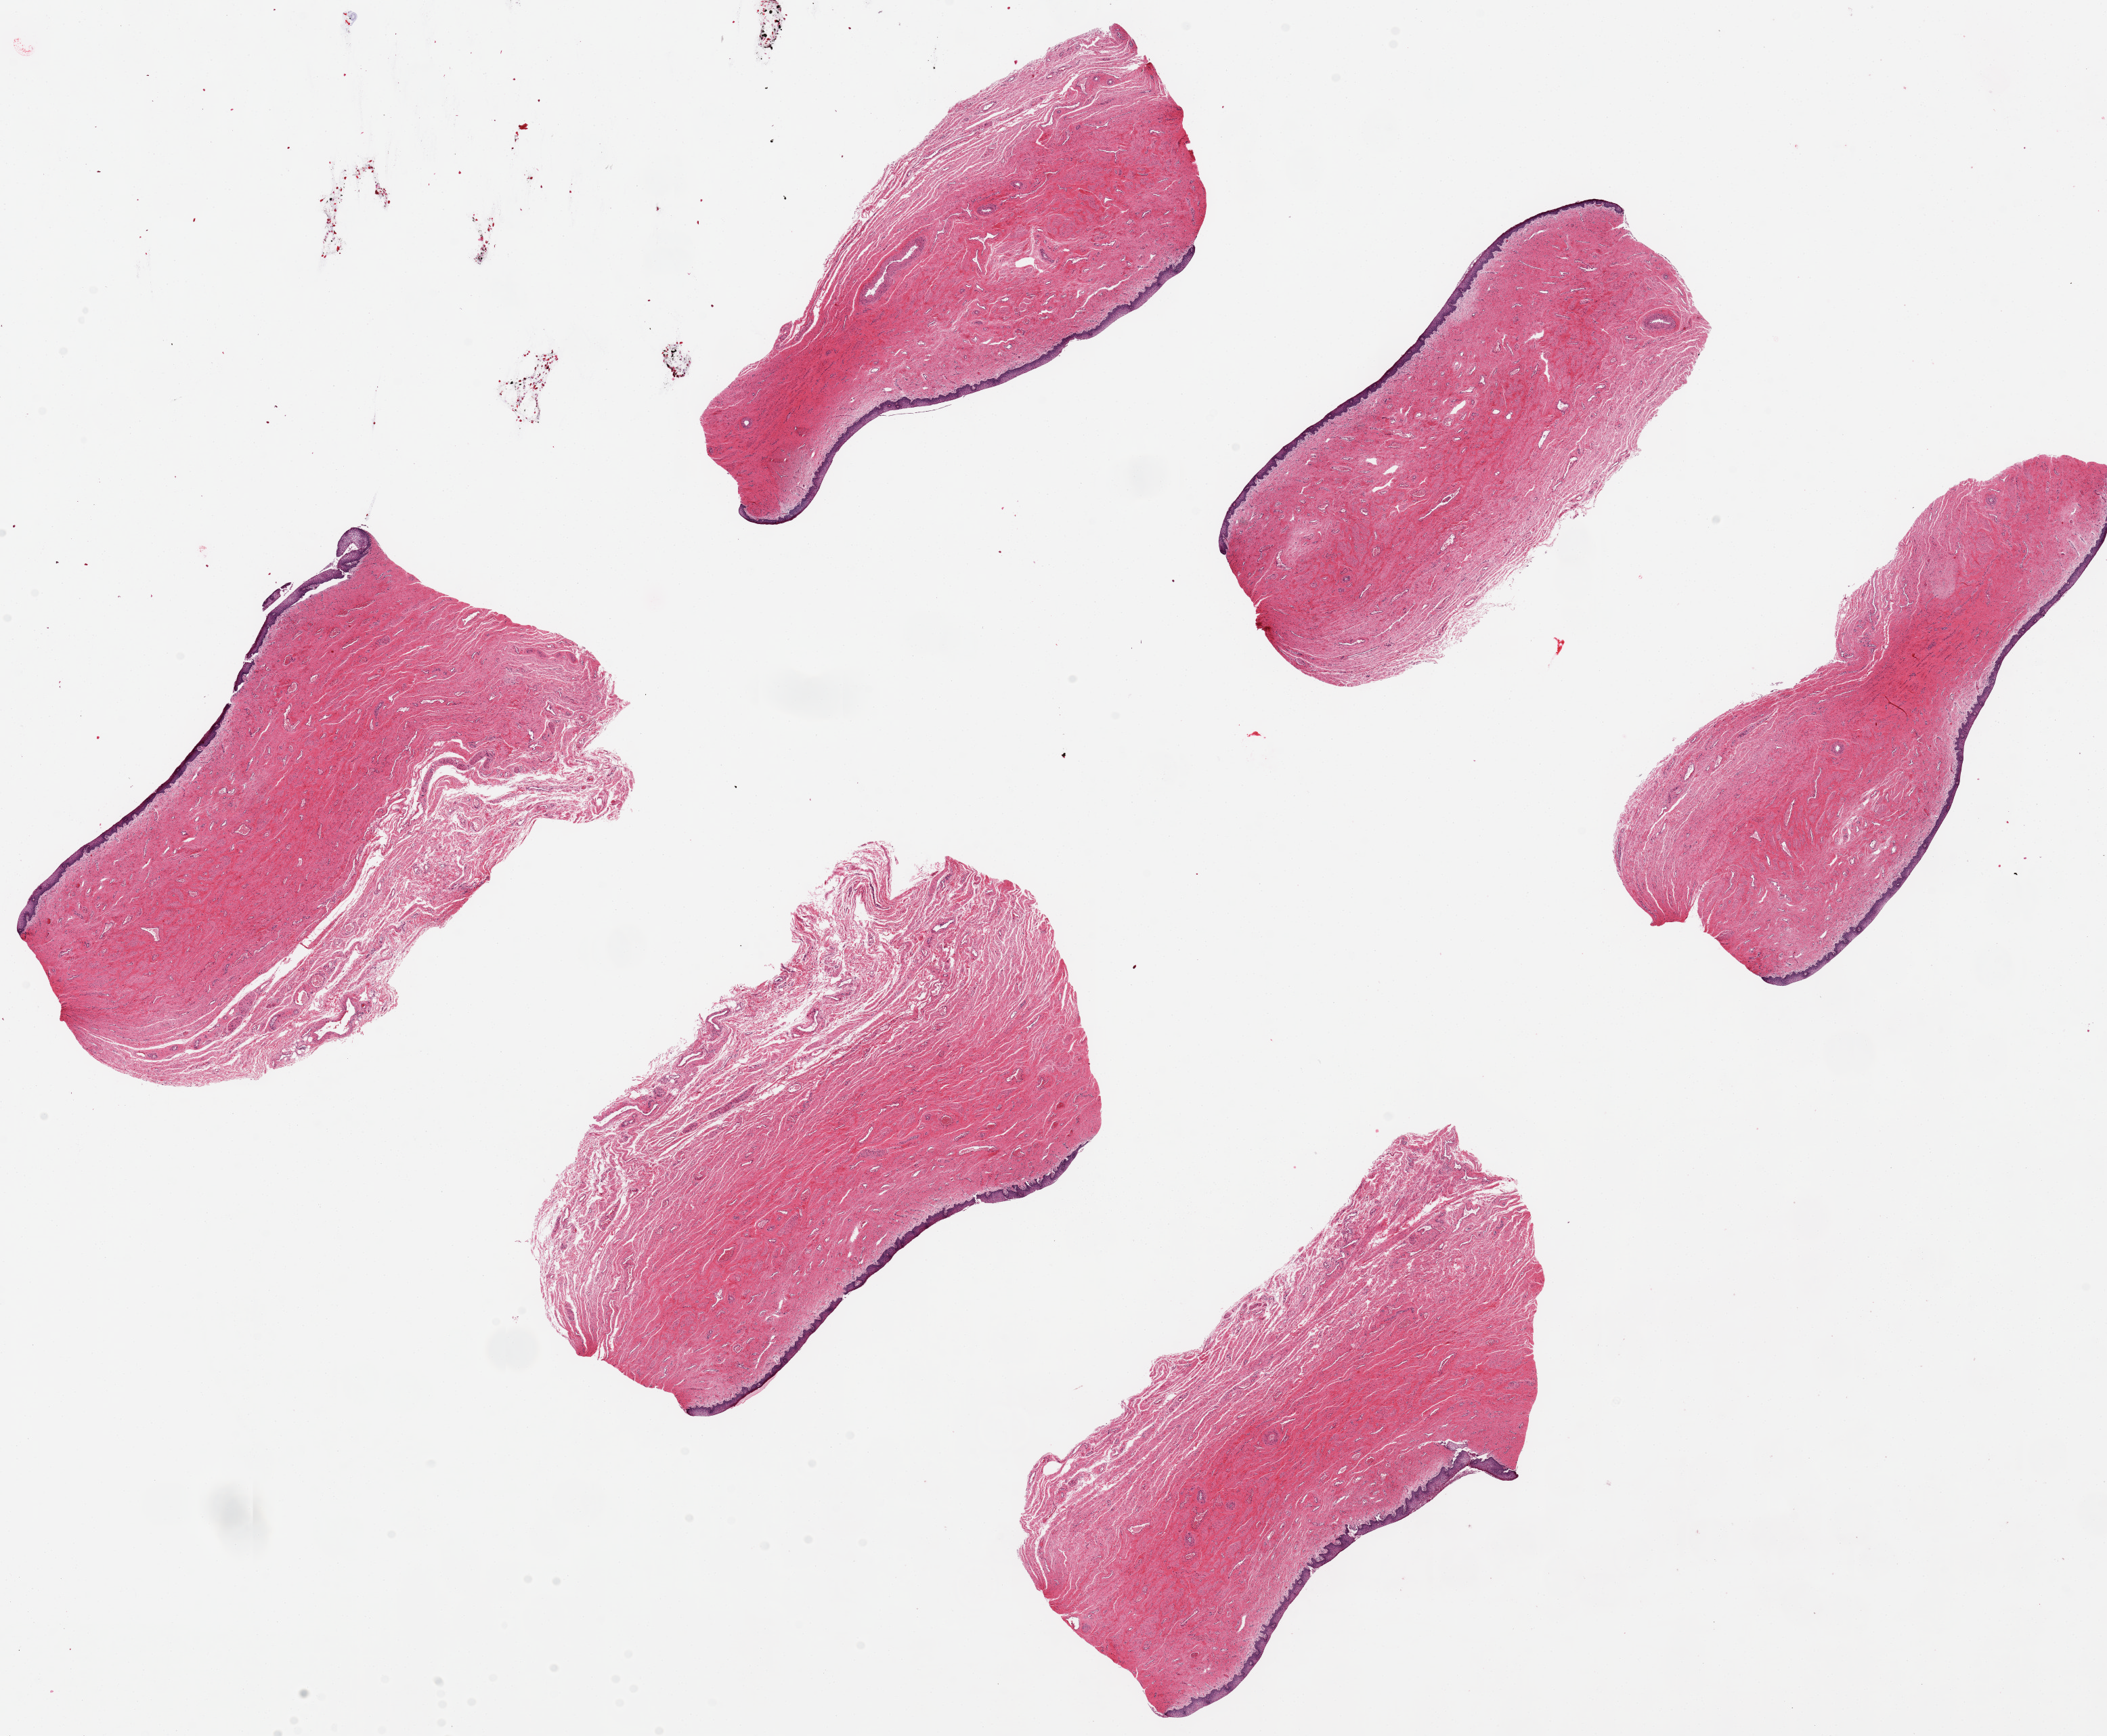
Hematoxylin and eosin (H&E) whole-slide image, low-resolution overview of the scanned area, about 24.6 x 20.3 mm, PAXgene-fixed paraffin-embedded (PFPE) section, target tissue: vagina, tissue donor sample. Donor: female.
Review note (as recorded): 6 ~7x3mm pieces; squamous mucosa, focally beginning to slough, is ~2-3% of thickness.